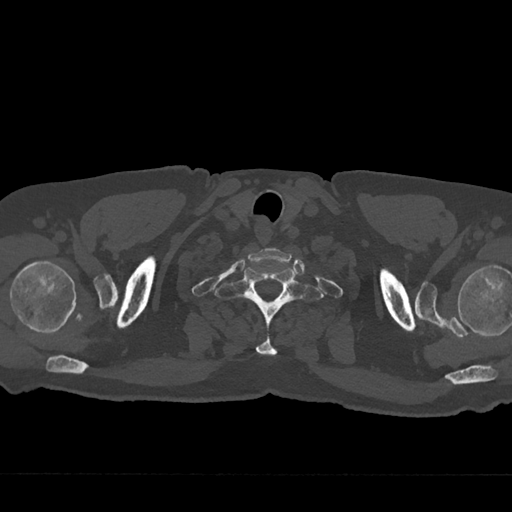
CT including the spine, one axial slice. Slice 665 of 797 in the series (ordered by position). Reconstruction kernel Br40s/3. 120 kVp. Bone window (W 1800 / L 400 HU). 512 × 512 image matrix, field of view 377 × 377 mm. Male patient, age 75 years. From the clinical record (not read from this slice): primary cancer: renal; vertebrae with lytic lesions (as recorded): T4.
Outlined on this slice (semi-automatically segmented with operator editing):
- T1 vertebra: bounding box [x1, y1, x2, y2] px = [215, 267, 323, 356]